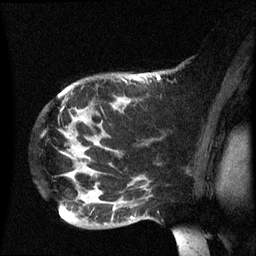
Breast MRI (dynamic contrast-enhanced), one sagittal slice. Slice 47 of 60 in the series (ordered by position). Dynamic contrast-enhanced series, image 2 of 3 at this slice position (ordered by acquisition). 1.5 T. TE 4.2 ms, TR 8.4 ms. 2.5 mm slice thickness. 256 × 256 image matrix, field of view 220 × 220 mm. Patient: female, 49 years.
Structures marked on this image (semi-automatically segmented with operator editing):
- analysis volume of interest (the breast-tissue region the enhancement analysis was run in; not a lesion): bounding box (x1, y1, x2, y2) in pixels: (59, 72, 185, 235)
- tumour enhancement mask (voxels above the 70 % enhancement threshold inside the analysis volume of interest): (132, 78, 140, 217)